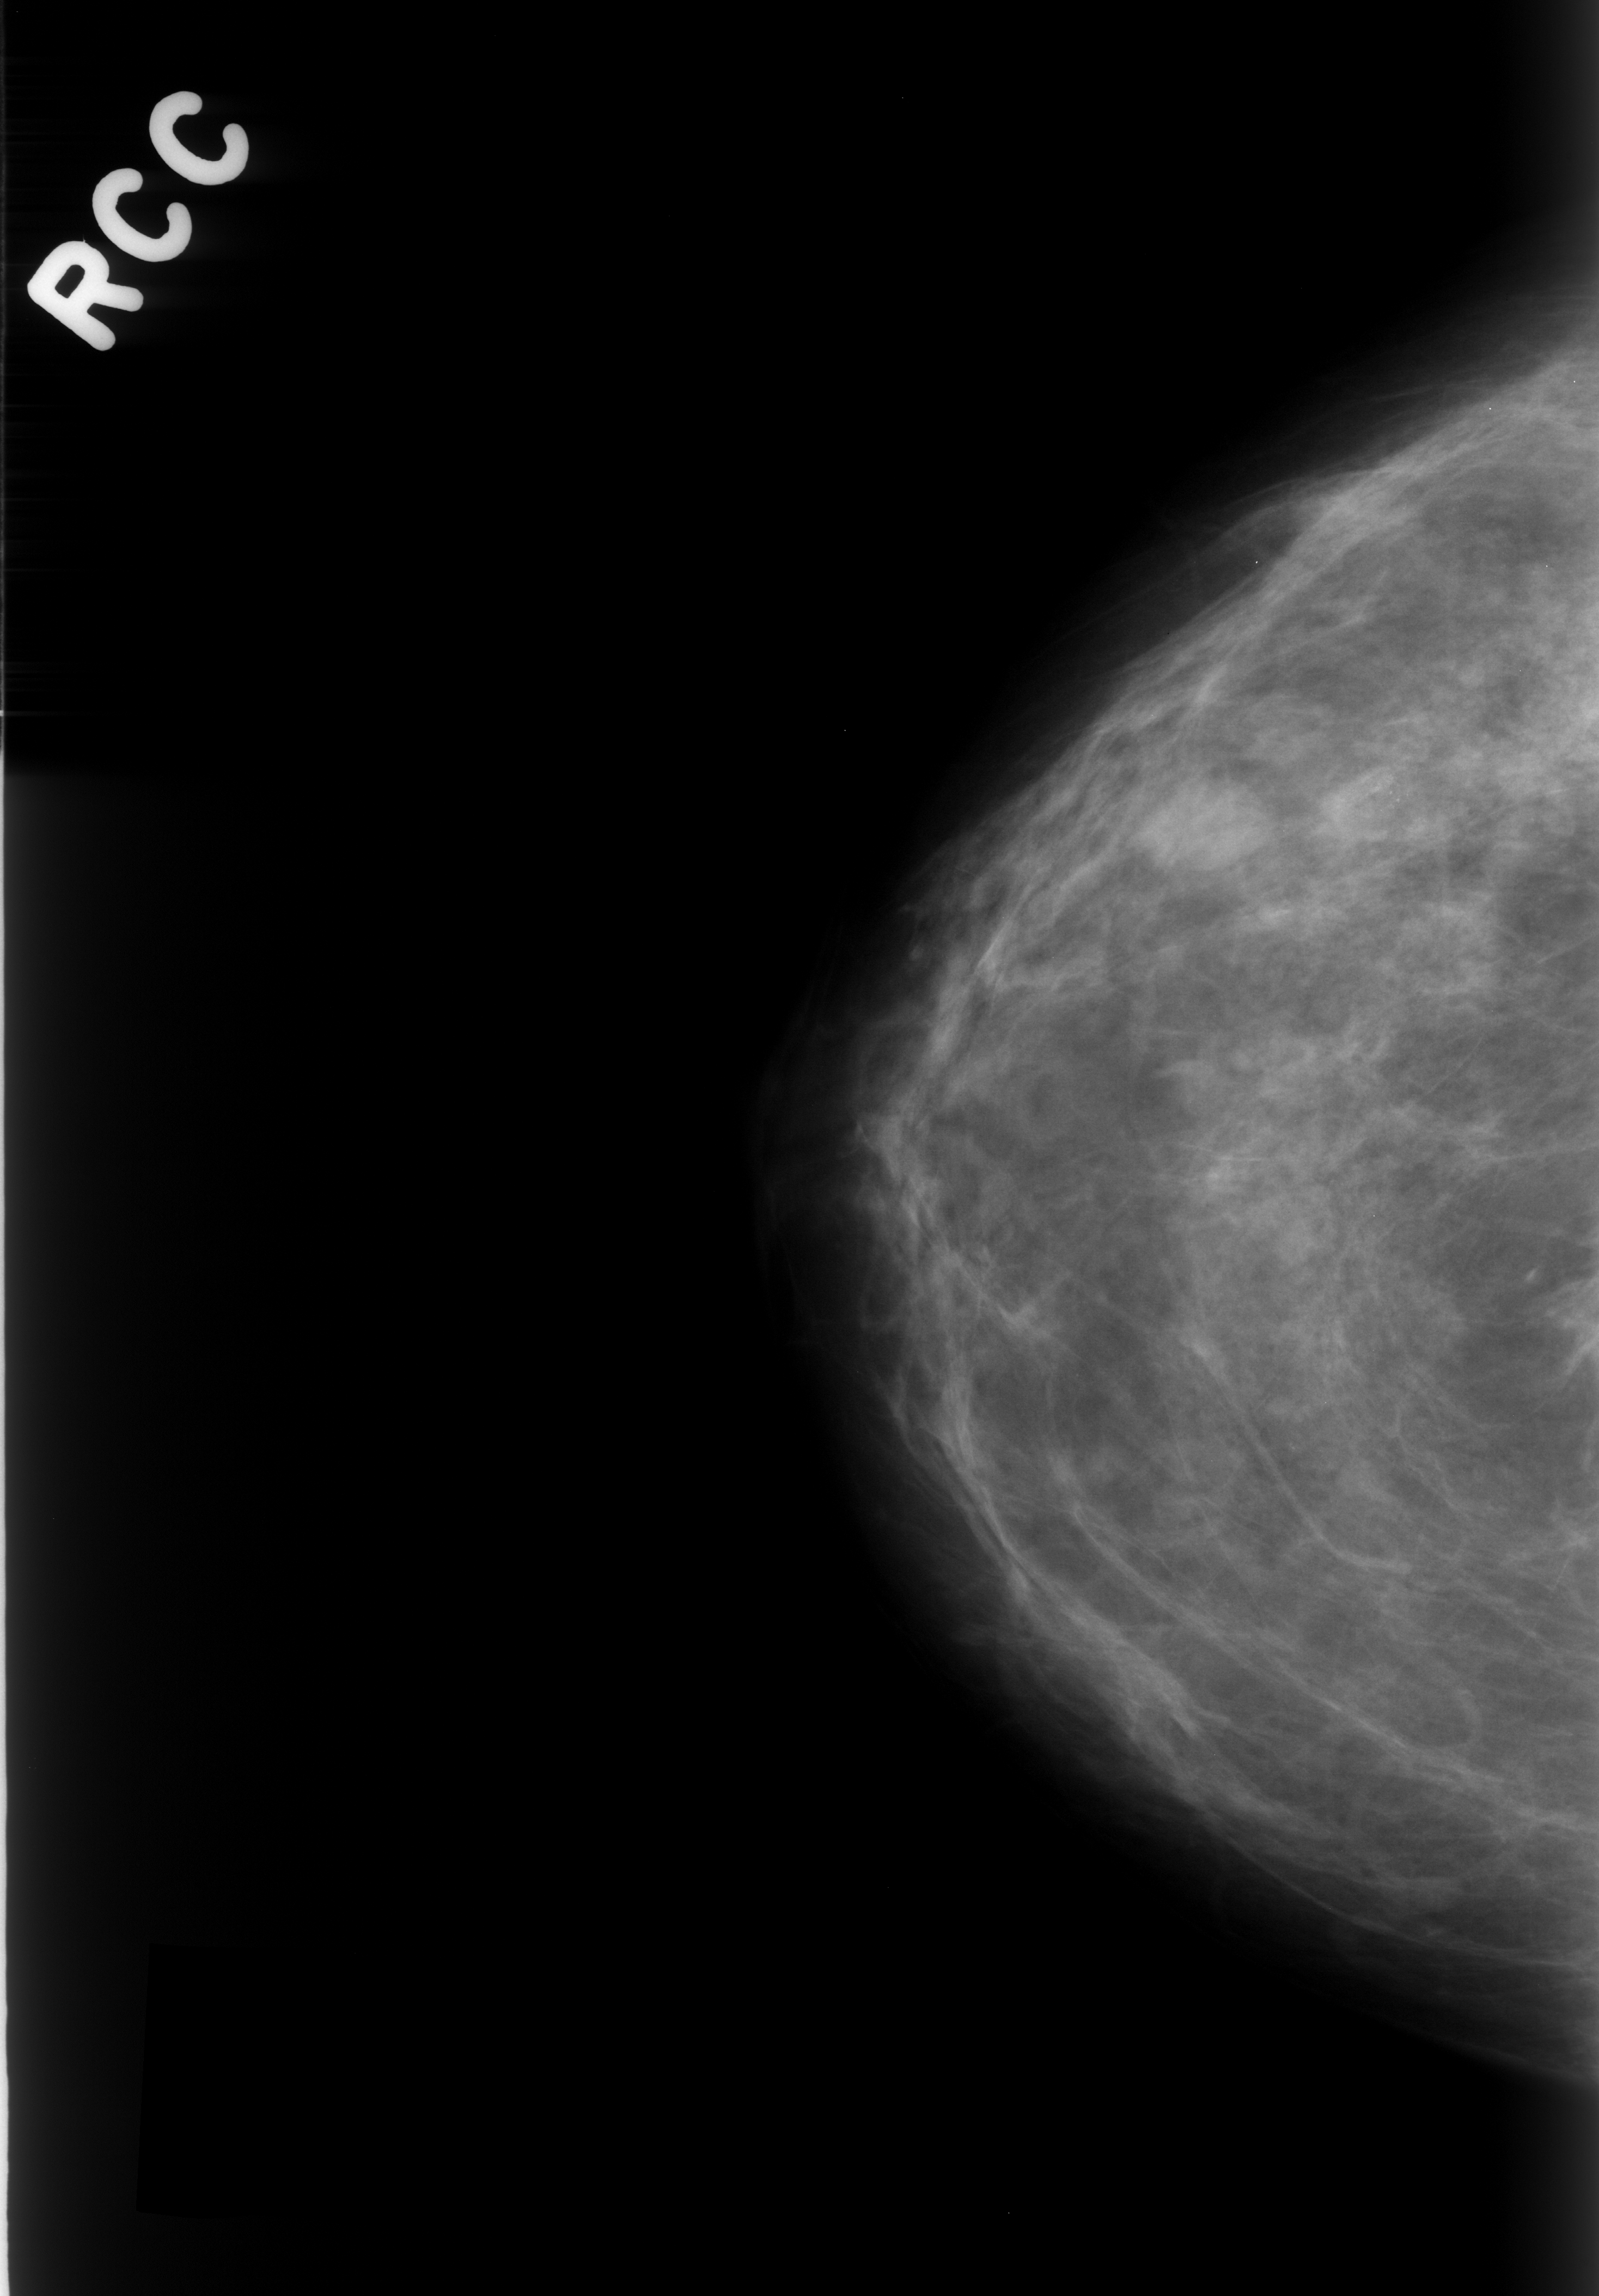
Scanned film-screen mammogram, right breast, craniocaudal (CC) view, breast composition: scattered fibroglandular densities (BI-RADS density category 2 of 4).
- Radiologist-marked abnormalities on this image: mass, shape oval, margins circumscribed; BI-RADS assessment category 3; pathology (as recorded): benign.